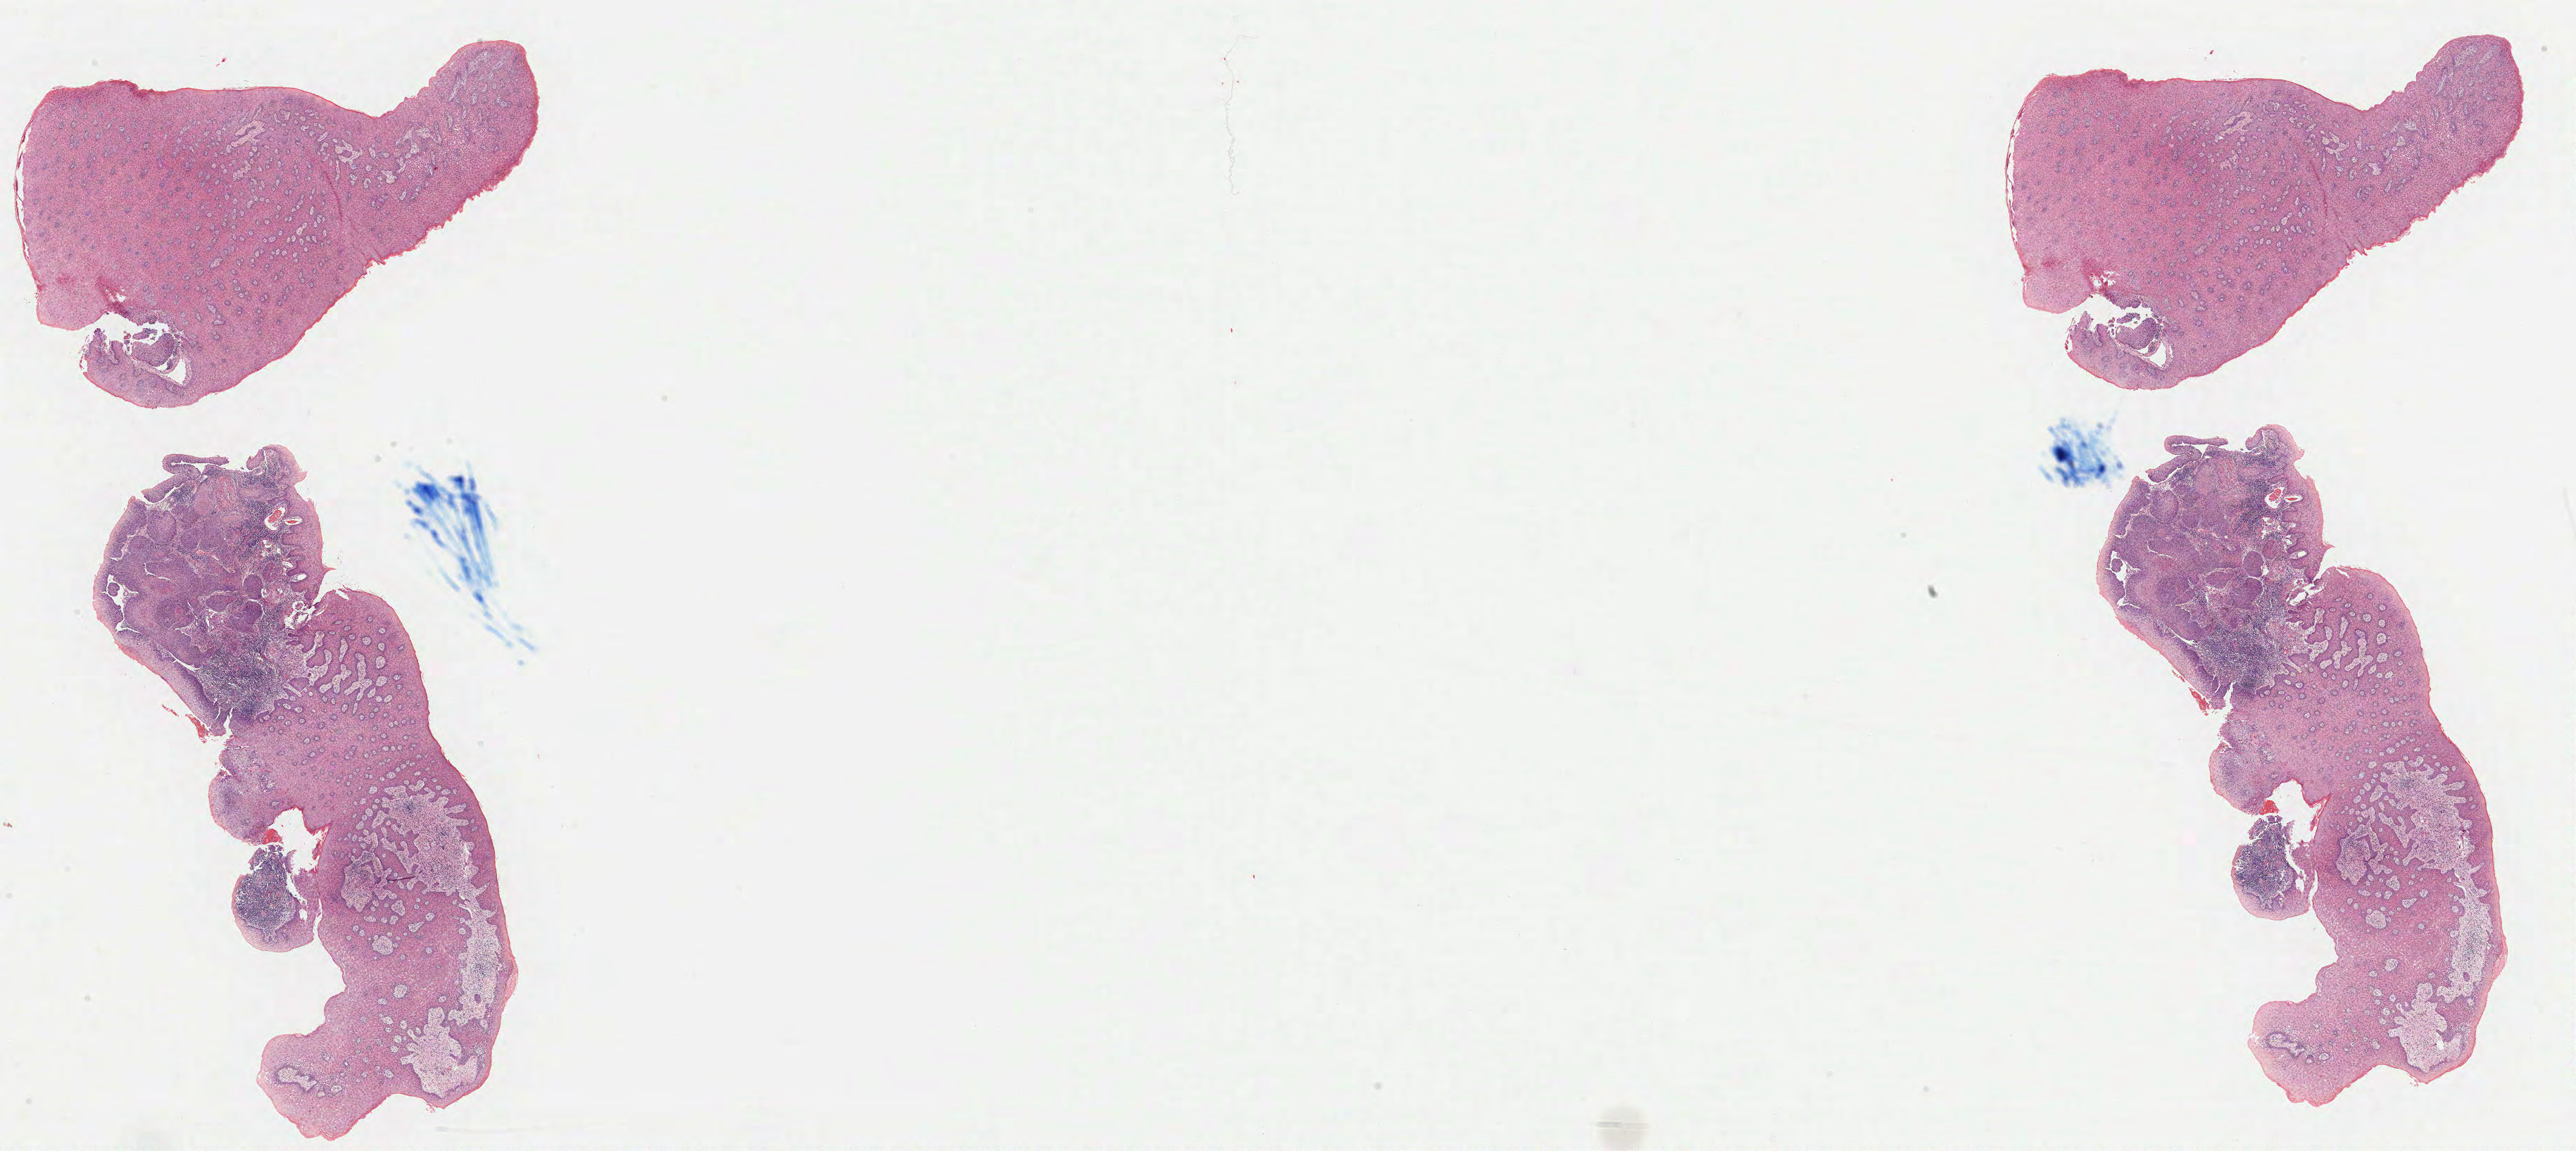
H&E-stained whole-slide image, a low-resolution overview of the entire scanned area, about 29.0 x 13.0 mm; formalin-fixed paraffin-embedded (FFPE) diagnostic section; cervix, primary tumour sample. Female patient; age at initial diagnosis 44 years. Histologic grade: G1 (well differentiated).
* lymph nodes positive (case pathology): 8 of 9 examined
* diagnosis: Squamous cell carcinoma, NOS (cervix uteri)
* FIGO stage: IIIB